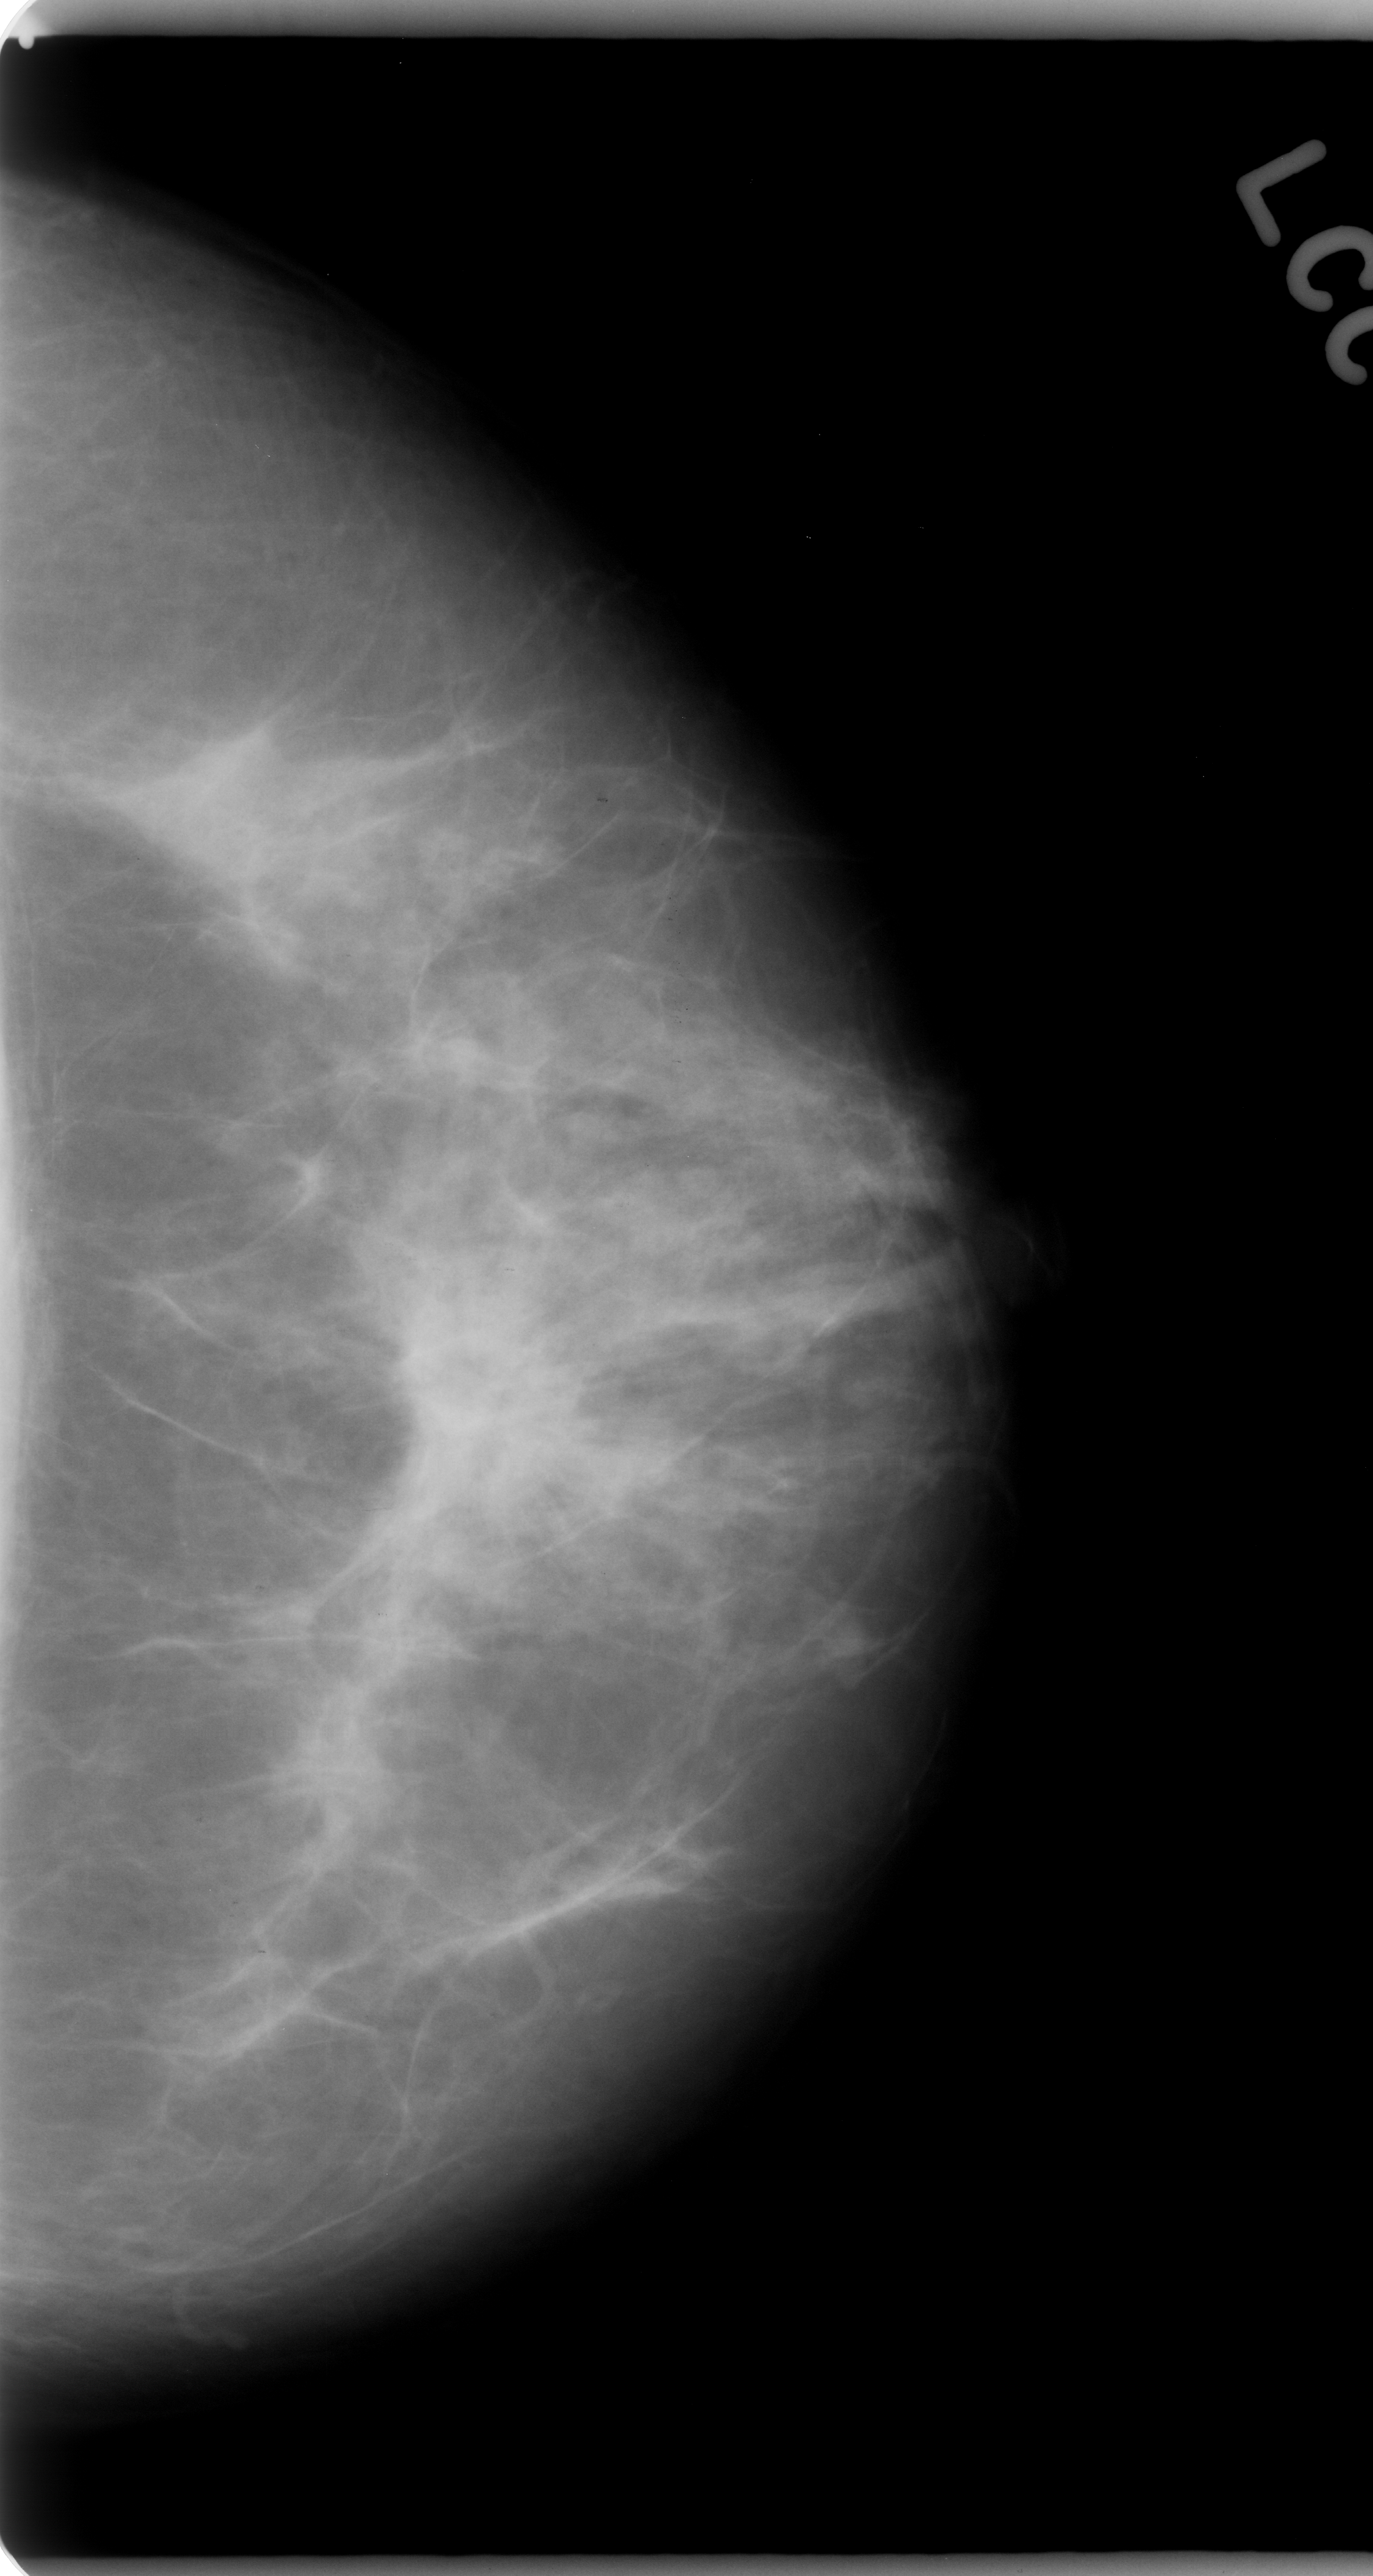
Scanned film-screen mammogram; left breast; CC view; BI-RADS breast density category 2 (scale 1–4); 1373 × 2576 image matrix.
Expert-marked regions of interest on this image (one box per marked abnormality):
- mass, shape architectural distortion, margins spiculated; BI-RADS assessment category 5; subtlety rating 5 on a 1 (subtle) to 5 (obvious) scale; pathology (as recorded): malignant: bounding box (x1, y1, x2, y2) in pixels: (362, 1230, 604, 1497)